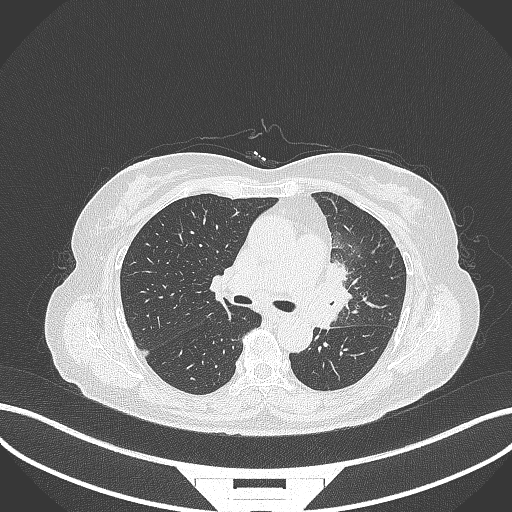
Chest CT, one axial slice; lung window (W 1500 / L -600 HU); 512 × 512 image matrix, field of view 400 × 400 mm. Patient: female, 64 years. Case-level facts recorded for this patient, not image findings: clinical TNM (as recorded): T2a N2 M0.
Annotated regions visible in this slice (bounding box drawn by a radiologist):
- lung tumour (recorded histology: adenocarcinoma): box from (x=323, y=258) to (x=365, y=331) px